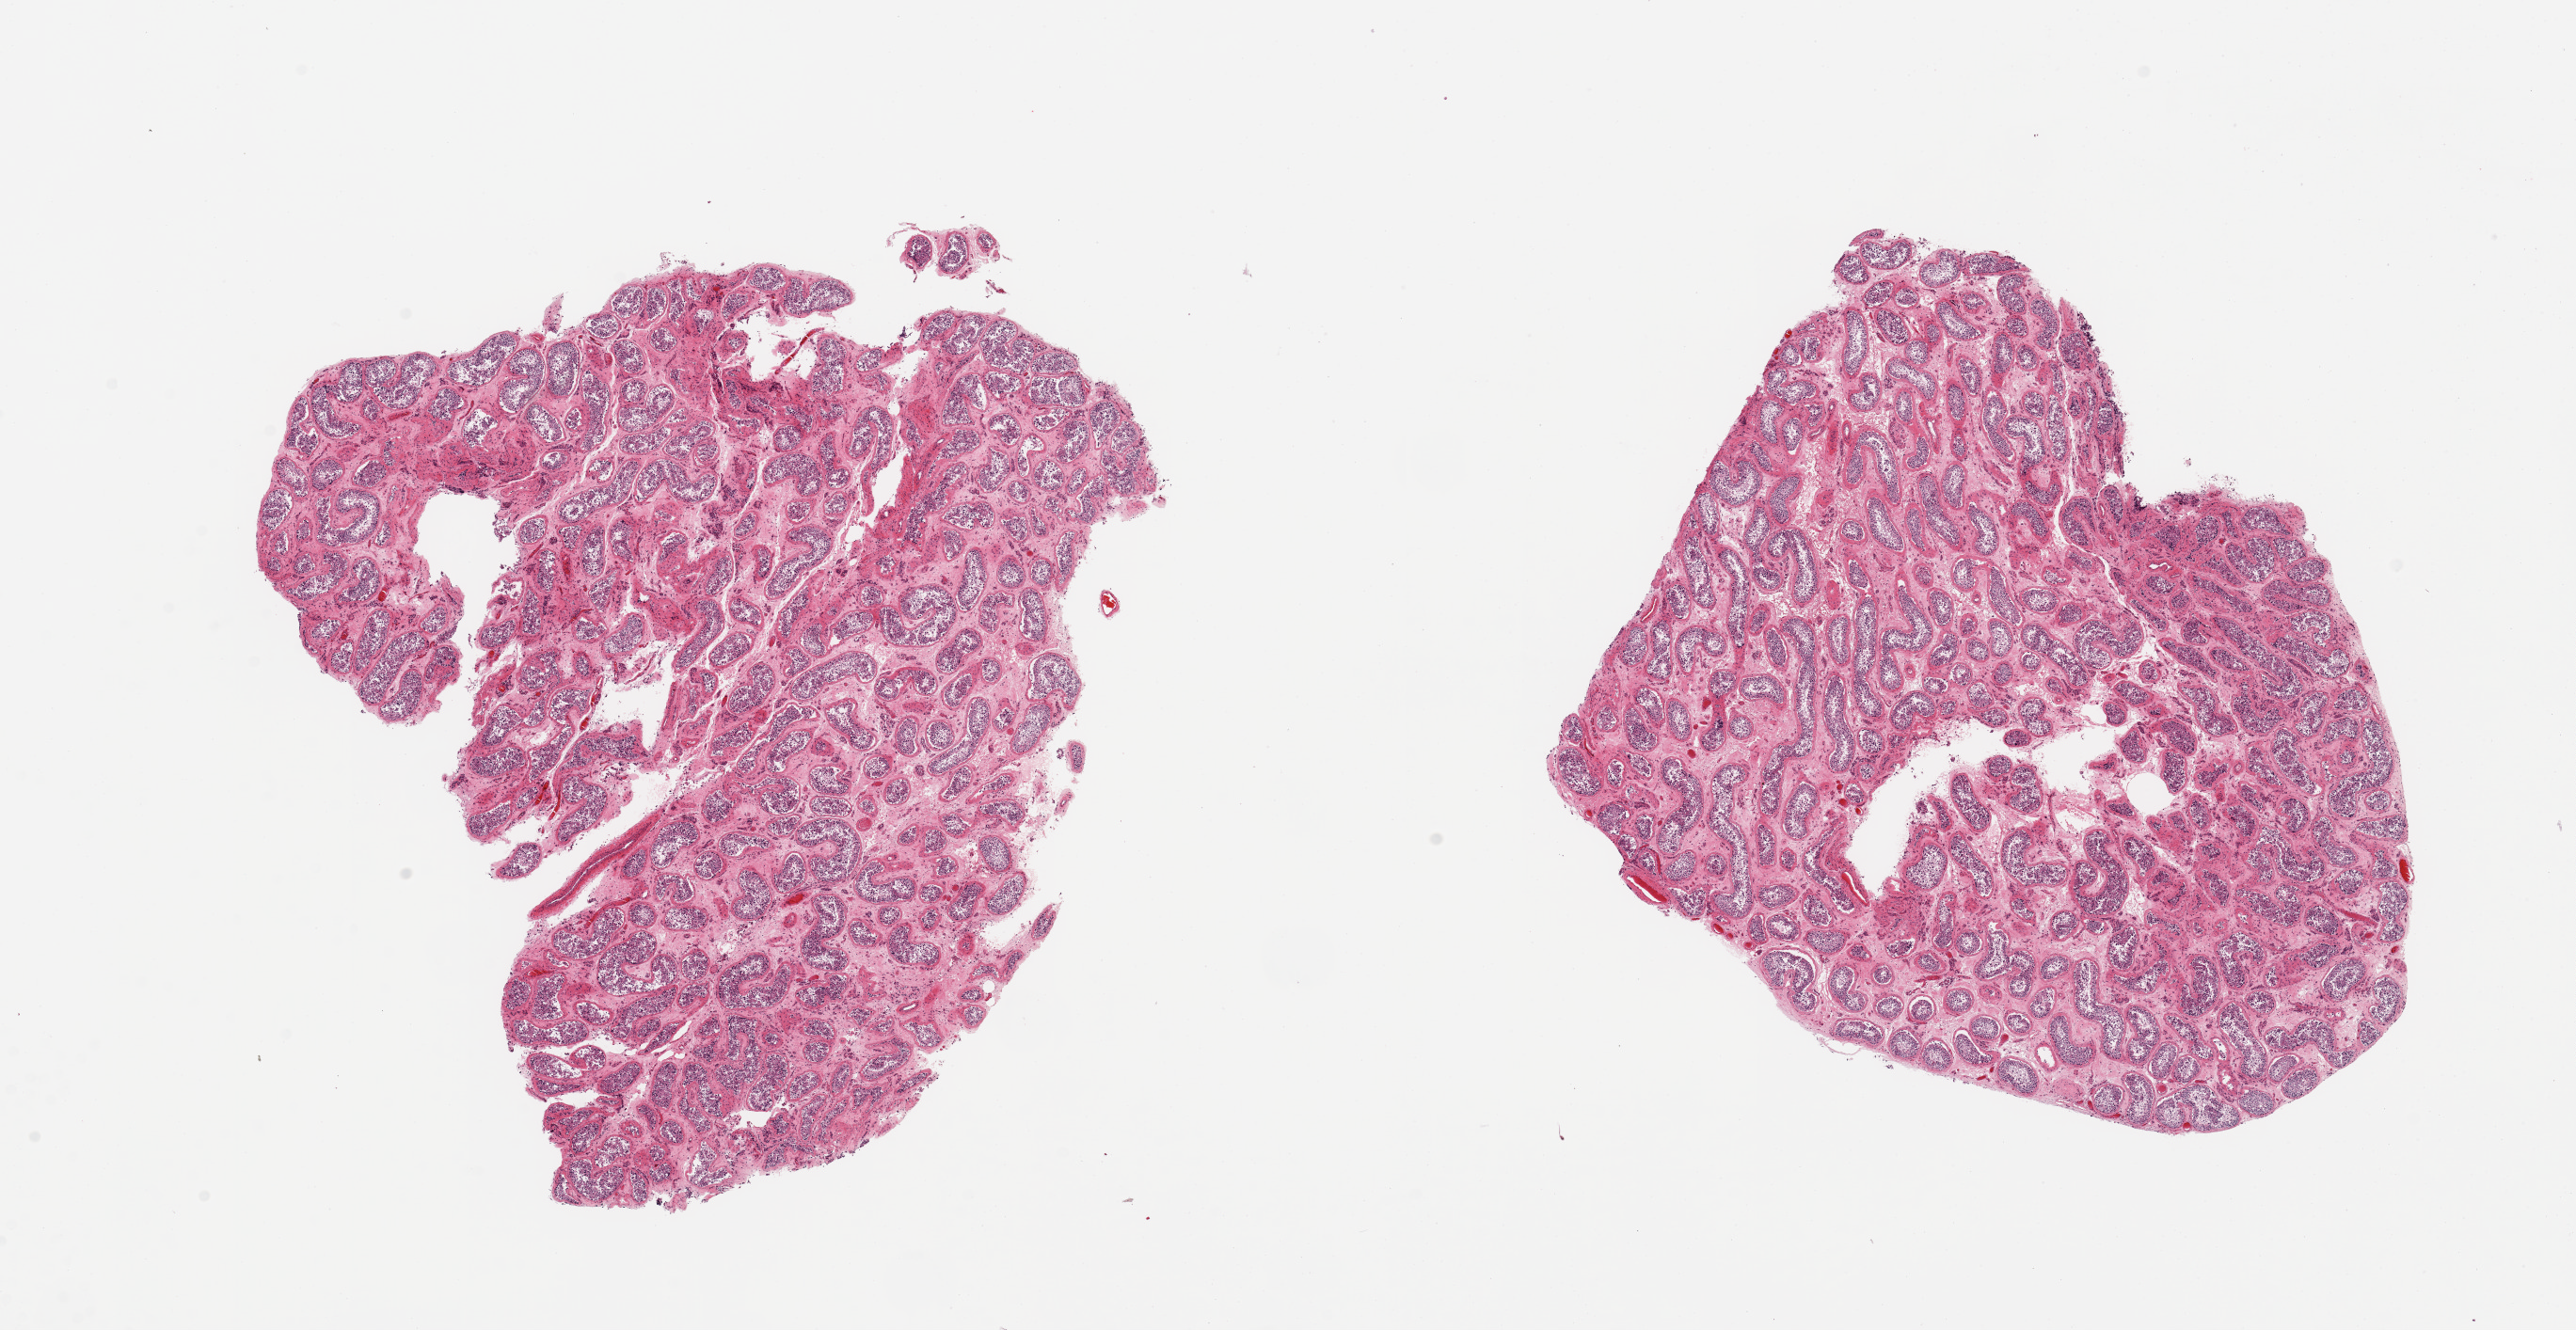
Digitized haematoxylin and eosin-stained section, brightfield — a low-resolution overview of the entire scanned area, about 21.7 x 11.2 mm; PAXgene-fixed paraffin-embedded (PFPE) section; section of testis (target tissue); tissue donor sample. Donor sex: male.
Pathologist's review note for this sample: 2 pieces; mildly reduced spermatogenesis.